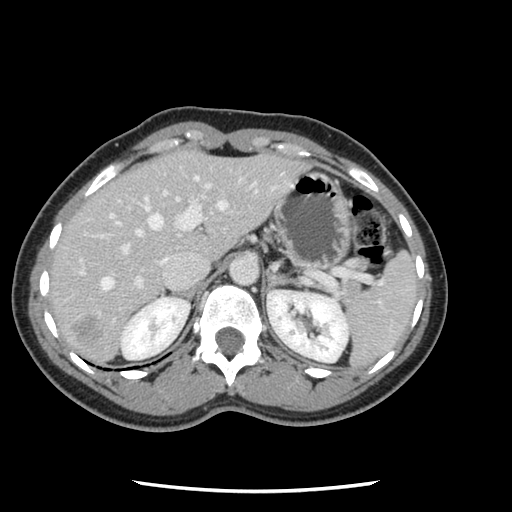
Contrast-enhanced abdominal CT, one axial slice. Slice 83 of 134 in the series (ordered by position). 120 kVp. Soft-tissue window (W 400 / L 40 HU). 512 × 512 image matrix, field of view 330 × 330 mm. Female patient, age 43 years. Case-level facts recorded for this patient, not image findings: diagnosis: colorectal cancer liver metastases, imaged before liver resection; multiple liver metastases: yes; largest metastasis: 3.4 cm; disease in both lobes: yes.
Annotated regions visible in this slice (outlined manually by an expert reader):
- hepatic veins: bounding box (x1, y1, x2, y2) in pixels: (80, 176, 228, 291)
- liver: (49, 152, 304, 364)
- planned liver remnant (the part of the liver to remain after resection): (49, 155, 190, 307)
- portal vein (with intrahepatic branches): (108, 184, 276, 290)
- liver metastasis: (75, 317, 102, 347)